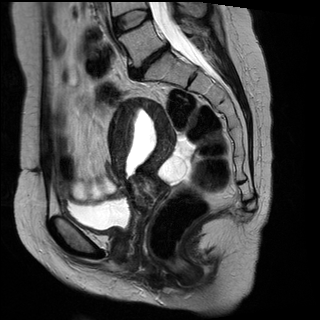
Pelvic MRI for cervical cancer, one sagittal slice; slice 15 of 29 in the series (ordered by position); T2-weighted; 1.5 T; TE 89 ms, TR 2930 ms; 4 mm slice thickness; 320 × 320 image matrix. Female patient, age 45 years.
Outlined on this slice (manually delineated by an expert):
- uterus and cervix: bounding box [x1, y1, x2, y2] px = [109, 98, 178, 215]